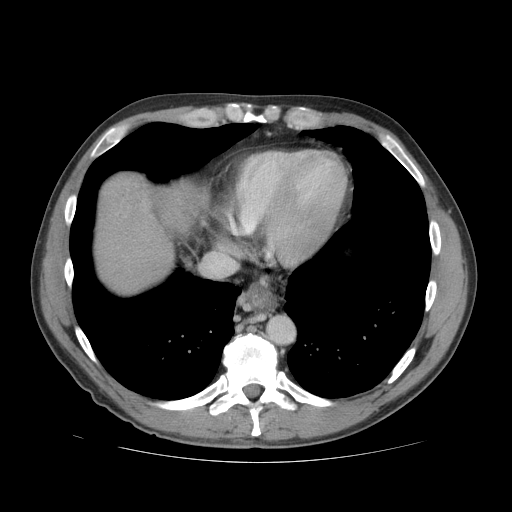
Contrast-enhanced abdominal CT (liver protocol), one axial slice. Position 71 of 81 along the scan axis. Reconstruction kernel STANDARD. 140 kVp. Soft-tissue window (W 400 / L 40 HU). 512 × 512 image matrix. From the clinical record (not read from this slice): diagnosis: hepatocellular carcinoma (patient treated with transarterial chemoembolisation; whether this scan precedes or follows treatment is not stated here); TNM stage (as recorded): Stage-IVB; Child-Pugh class: B; tumour differentiation: well differentiated; tumour nodularity: multinodular.
Annotated regions visible in this slice (semi-automatically segmented with operator editing):
- liver parenchyma outside the tumour (the mass and vessels are separate outlines, so this box may not span the whole liver): bounding box <94,172,206,292> (left, top, right, bottom; pixels)
- mass: <102,174,146,213>